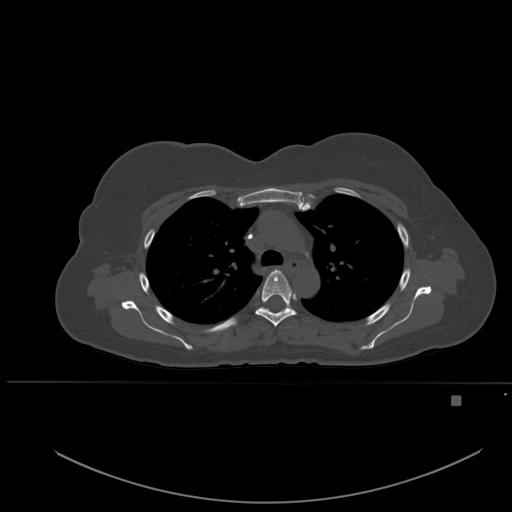
CT including the spine, one axial slice. Slice 379 of 651 in the series (ordered by position). Bone window (W 1800 / L 400 HU). 1.5 mm slice thickness. 512 × 512 image matrix, field of view 443 × 443 mm. Patient: female, 49 years. Case-level facts recorded for this patient, not image findings: primary cancer: breast.
Structures marked on this image (semi-automatic segmentation, software-assisted and operator-edited):
- T4 vertebra: bounding box <255,270,297,327> (left, top, right, bottom; pixels)
- T5 vertebra: <267,306,289,311>